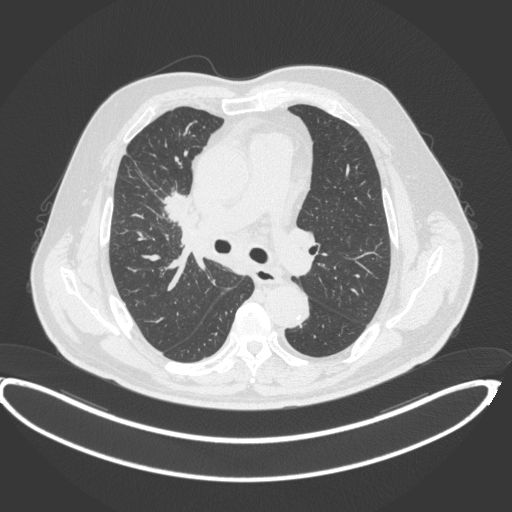
Chest CT, one axial slice. Slice 252 of 395 in the series (ordered by position). 120 kVp. Lung window (W 1500 / L -600 HU). 1 mm slice thickness. 512 × 512 image matrix. Patient: male, 62 years. Case-level facts recorded for this patient, not image findings: clinical TNM (as recorded): T1c N3 M1c.
Structures marked on this image (bounding box drawn by a radiologist):
- lung tumour (recorded histology: adenocarcinoma): bounding box [x1, y1, x2, y2] px = [161, 184, 201, 228]